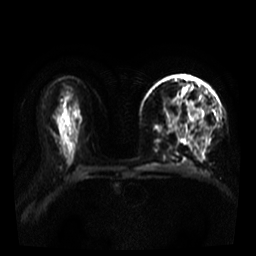
Breast MRI, one axial slice. Position 21 of 39 along the scan axis. Diffusion-weighted series; image 2 of 4 stored at this slice position (different b-values; order by instance number). 3 T. 256 × 256 image matrix, field of view 320 × 320 mm. Female patient.
Annotated regions visible in this slice (outlined manually by an expert reader):
- tumour on diffusion-weighted imaging: bounding box <171,98,204,125> (left, top, right, bottom; pixels)